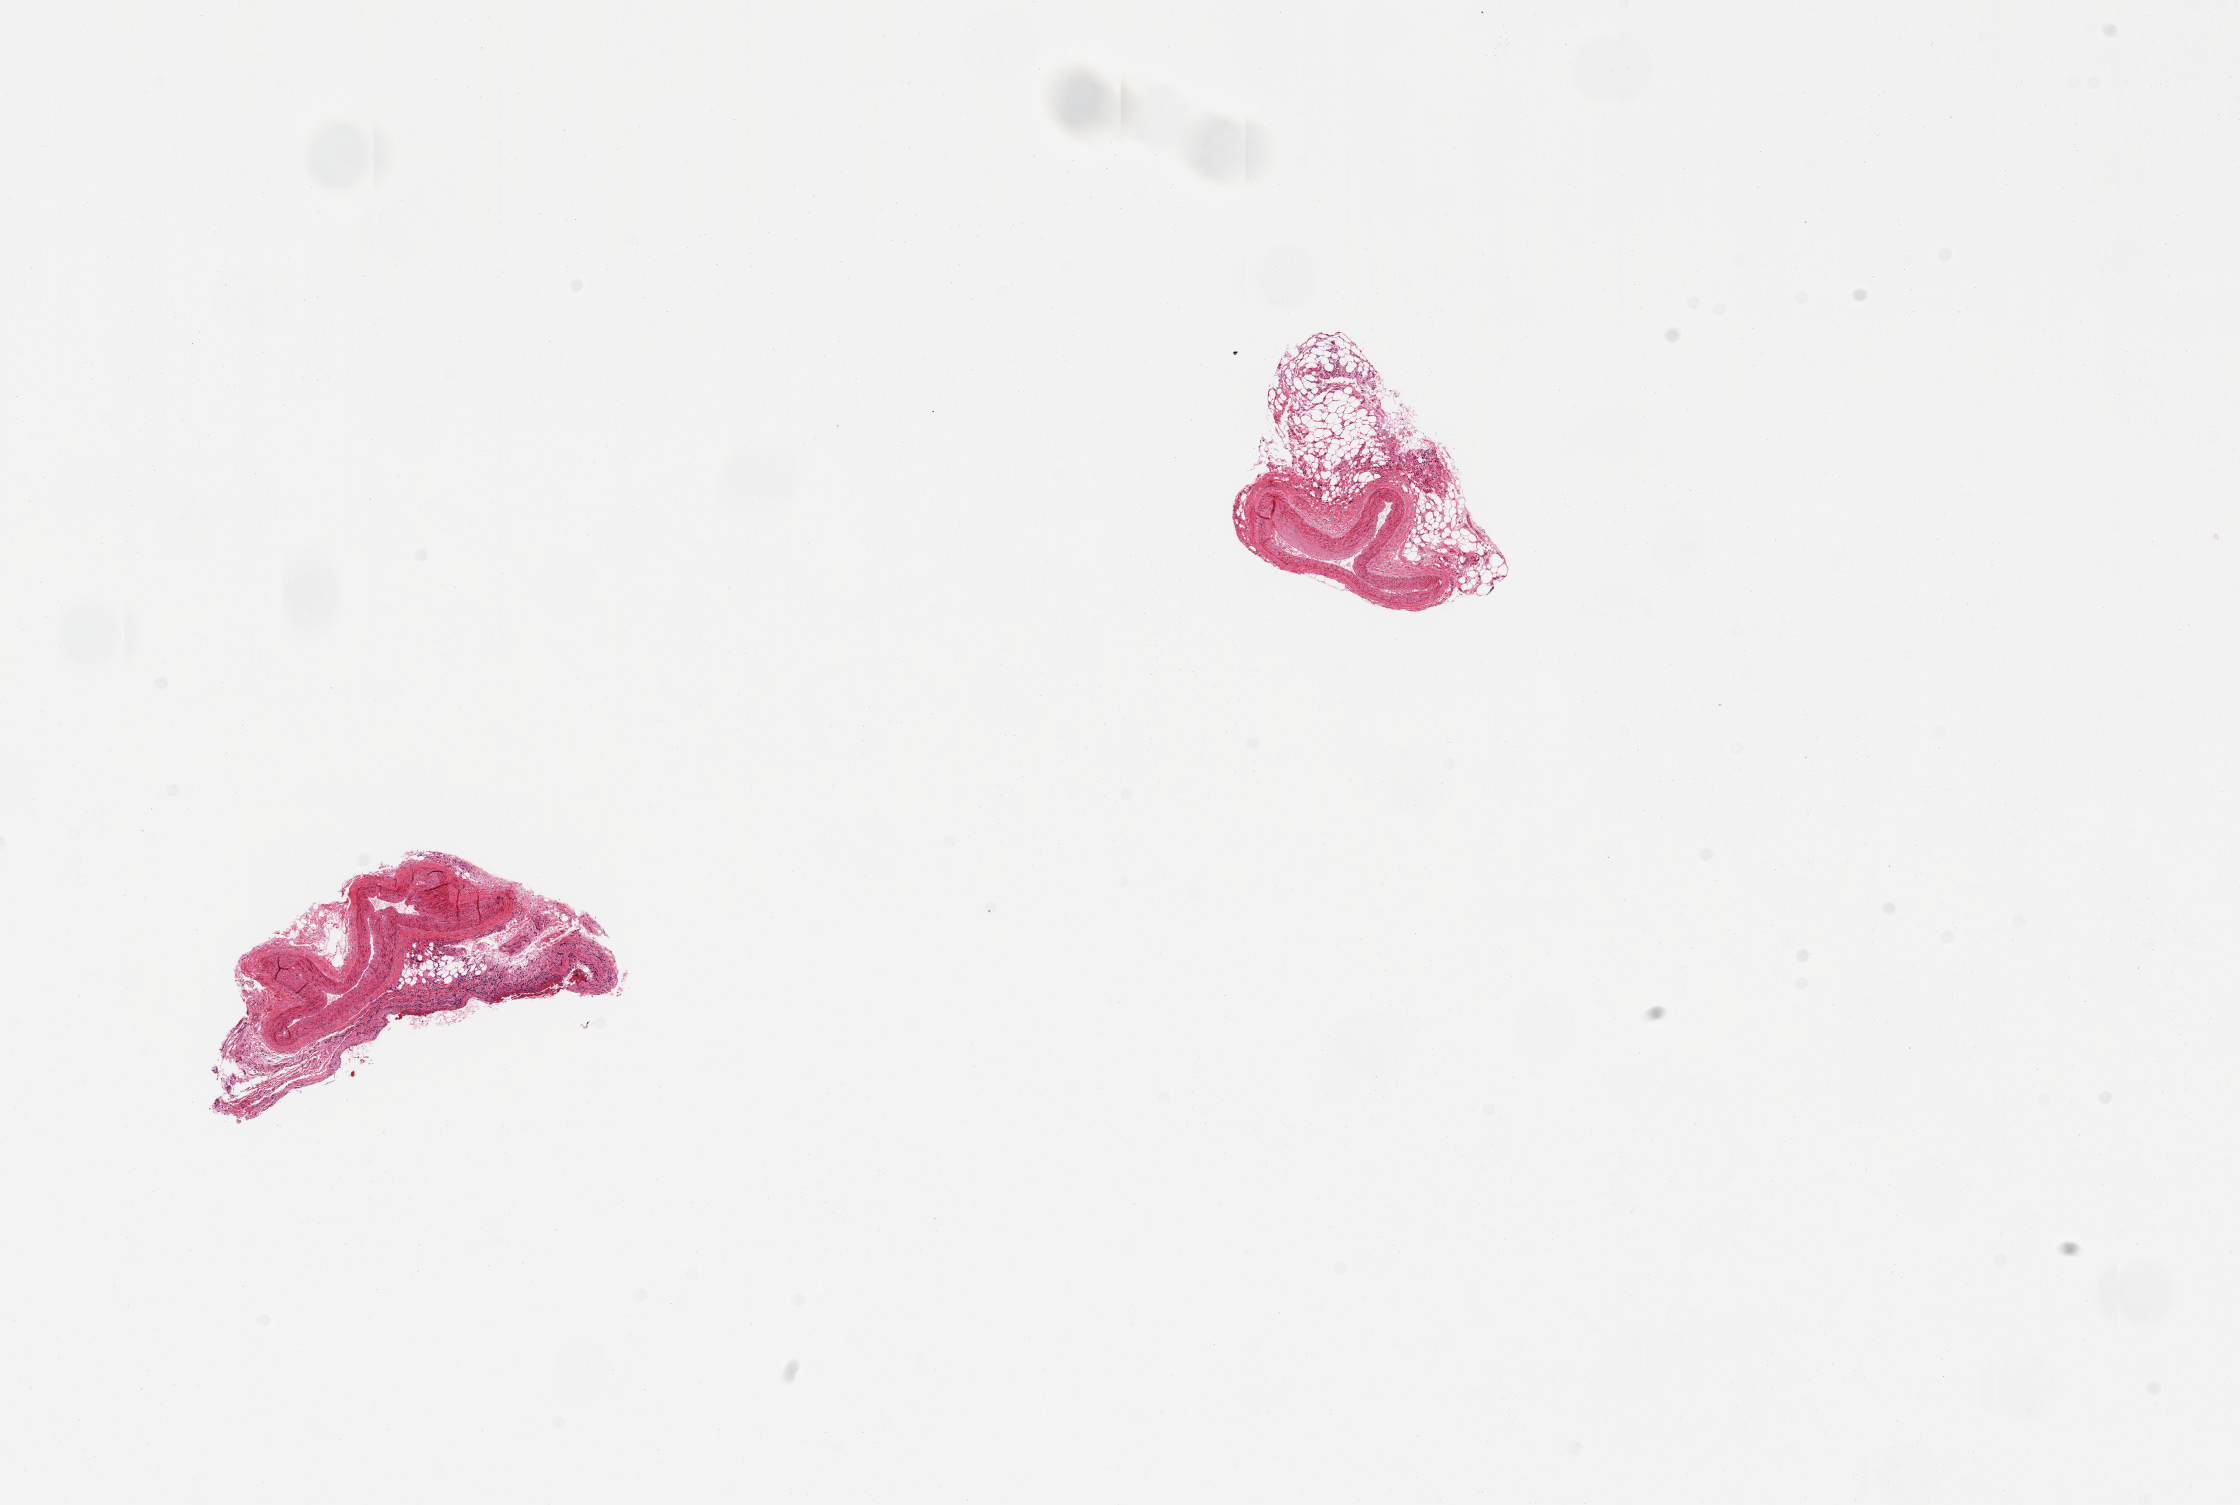
Haematoxylin and eosin whole-slide image, a low-resolution overview of the entire scanned area, about 17.7 x 11.9 mm (slide scanned at 20x), PAXgene-fixed paraffin-embedded (PFPE) section, sampled site (target tissue): coronary artery, tissue donor sample. Female donor.
- pathologist's review note for this sample: 2 pieces; 50% external fat